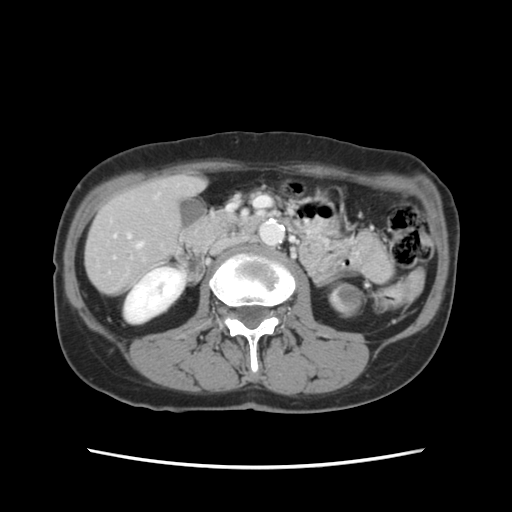
Contrast-enhanced abdominal CT, one axial slice; position 37 of 120 along the scan axis; intravenous contrast given; soft-tissue window (W 400 / L 40 HU); 2.5 mm slice thickness; 512 × 512 image matrix. Female patient, age 70 years. Case-level facts recorded for this patient, not image findings: diagnosis: colorectal cancer liver metastases, imaged before liver resection; multiple liver metastases: no; largest metastasis: 2.5 cm; disease in both lobes: no.
Outlined on this slice (expert manual segmentation):
- hepatic veins: bounding box [x1, y1, x2, y2] px = [137, 243, 142, 248]
- liver: [85, 177, 202, 293]
- planned liver remnant (the part of the liver to remain after resection): [85, 176, 203, 294]
- portal vein (with intrahepatic branches): [127, 234, 130, 238]